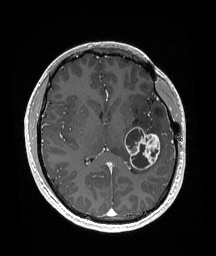
Brain MRI from a brain-tumour surgery series, one axial slice. Position 88 of 192 along the scan axis. T1-weighted post-contrast. 216 × 256 image matrix, field of view 211 × 250 mm. Case-level facts recorded for this patient, not image findings: histopathology: Glioneuronal tumor; WHO grade: 2; tumour location: Left Superior Temporal Gyrus.
Structures marked on this image (expert manual segmentation):
- tumour: box from (x=125, y=126) to (x=161, y=170) px